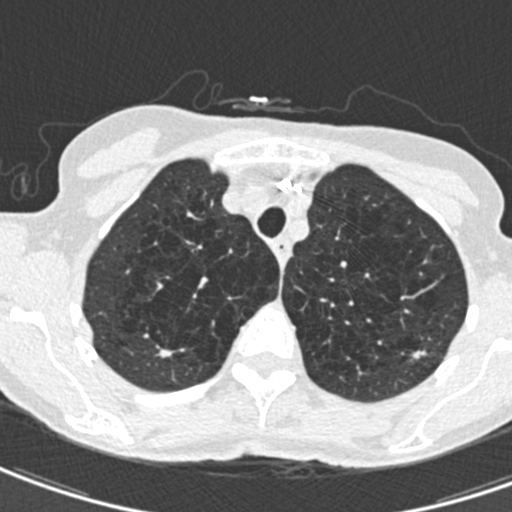
Low-dose screening chest CT, axial slice. Second screening round (one year after baseline). Lung window (W 1500 / L -600 HU). 0.75 mm slice thickness. Standard (soft-tissue) reconstruction kernel (B30f). 512 × 512 image matrix, field of view 272 × 272 mm. Female, age 71 years at enrolment. Current smoker at enrolment.
Expert-annotated lung lesion, bounding box <405,332,444,370> (left, top, right, bottom; pixels). The screening reader recorded 2 non-calcified nodules or masses ≥4 mm on this exam (right upper lobe, left upper lobe); which of them this box marks is not recorded. Lung cancer was diagnosed 604 days after this screen: adenocarcinoma, NOS, left upper lobe, moderately differentiated (G2), stage IA (AJCC 6th edition), 12 mm at pathology.